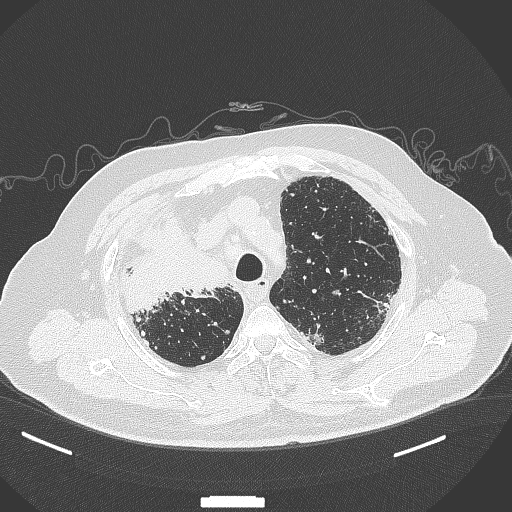
Chest CT, one axial slice. Position 286 of 384 along the scan axis. Reconstruction kernel B70f. Lung window (W 1500 / L -600 HU). 1 mm slice thickness. 512 × 512 image matrix, field of view 400 × 400 mm. Patient: male, 69 years. From the clinical record (not read from this slice): clinical TNM (as recorded): T4 N3 M1.
Outlined on this slice (bounding box drawn by a radiologist):
- lung tumour (recorded histology: adenocarcinoma): bounding box (x1, y1, x2, y2) in pixels: (126, 214, 230, 317)